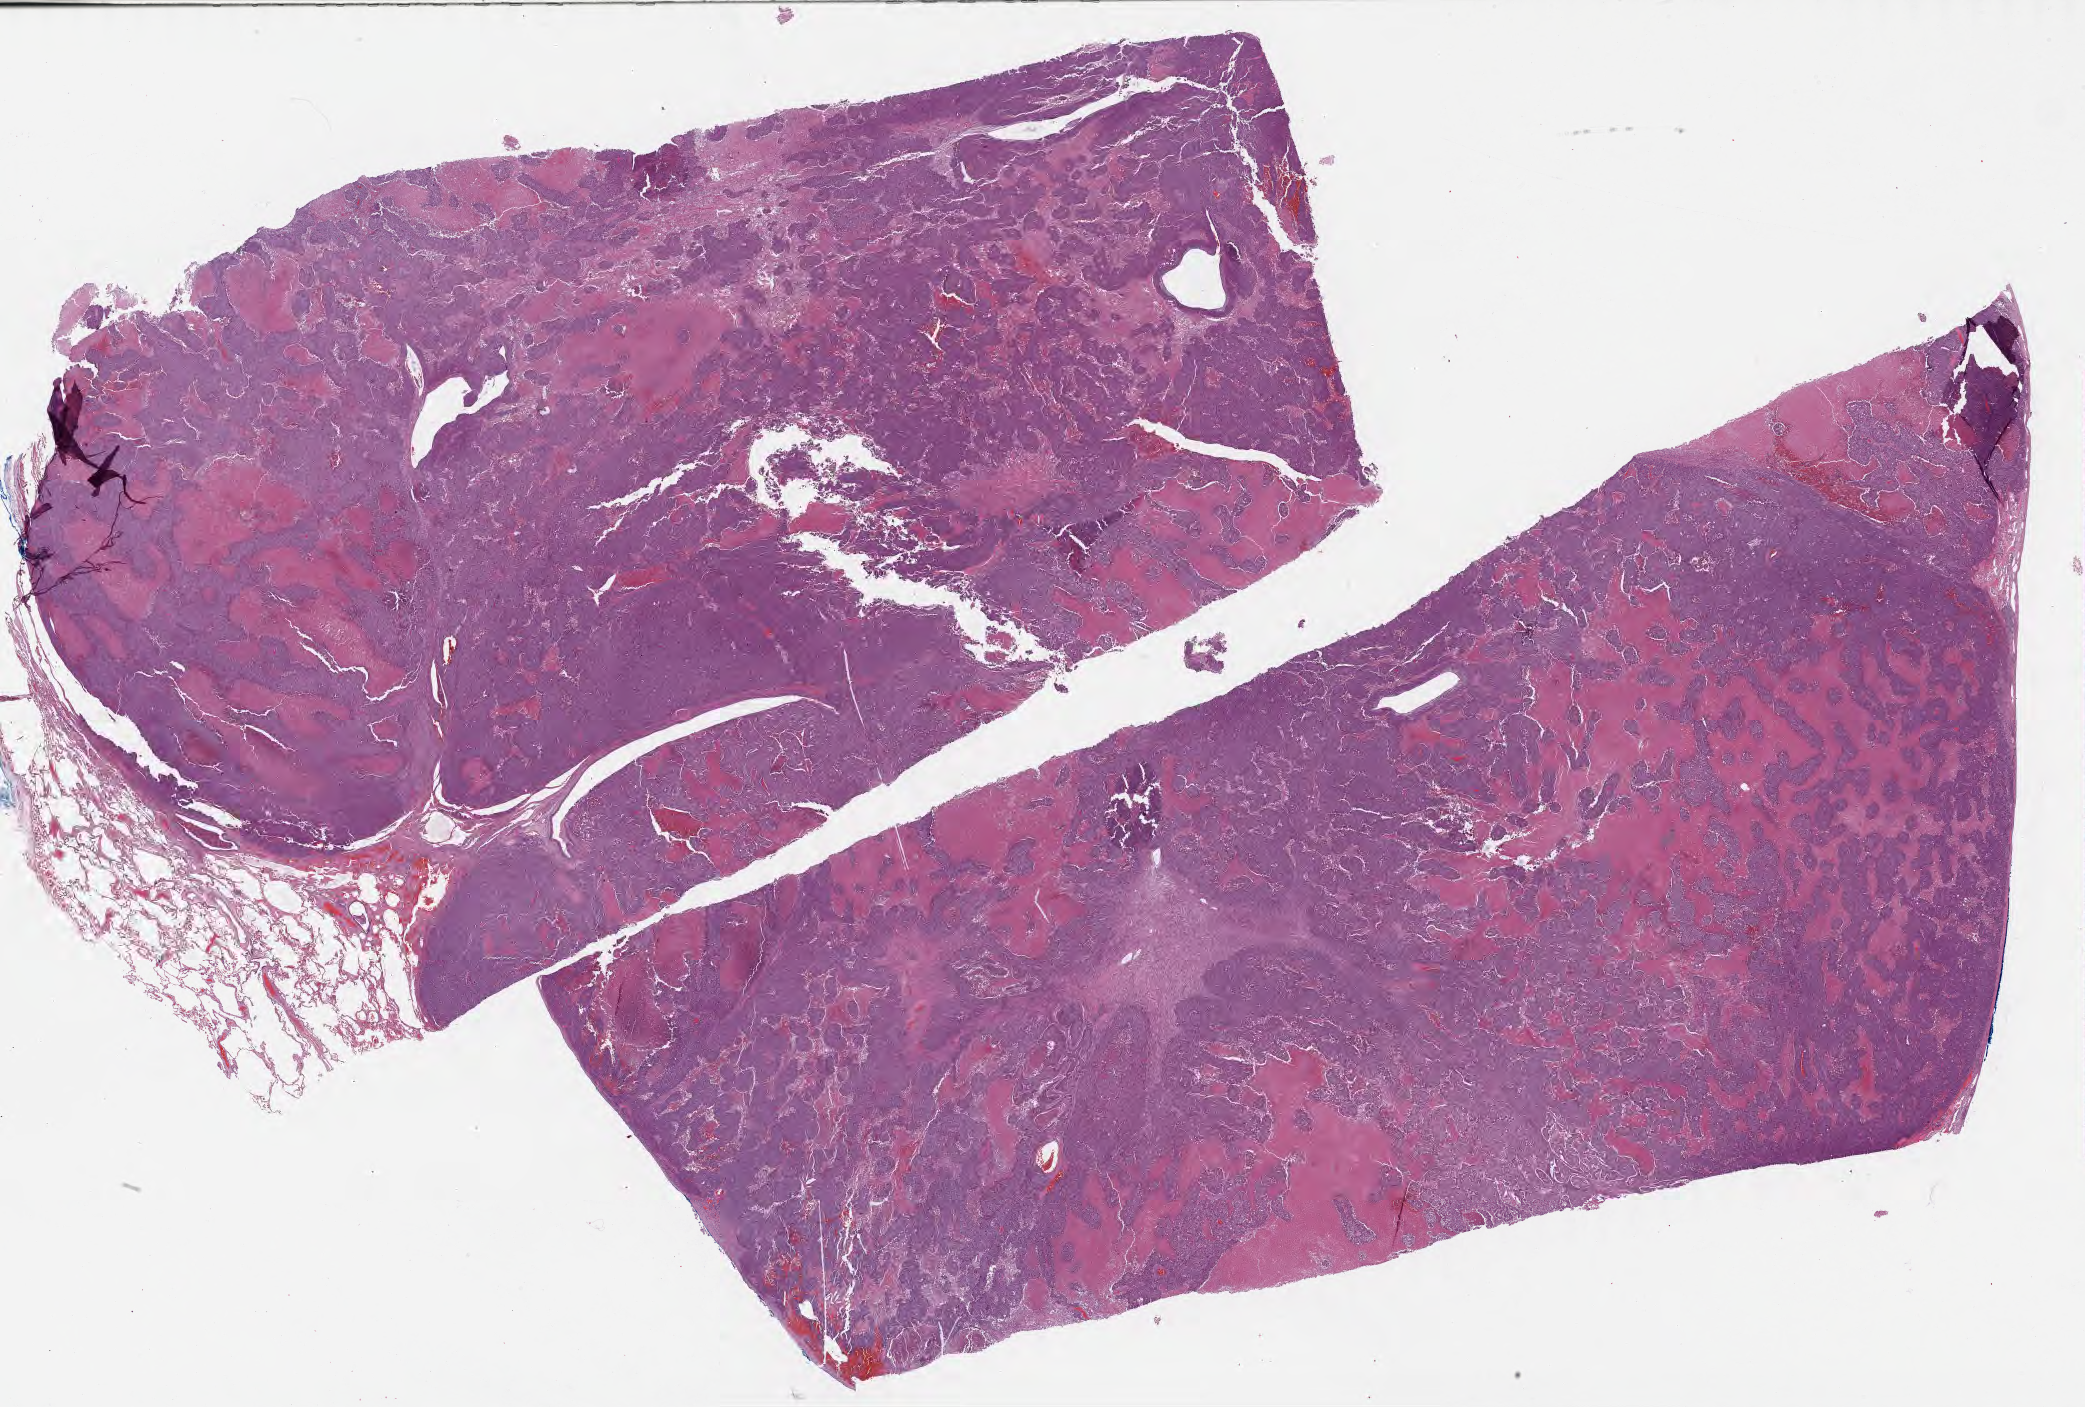
Haematoxylin and eosin whole-slide image, shown as a low-resolution overview of the whole scanned area (about 33.7 x 22.7 mm); tumor tissue; site: lung (right). Patient female; 61 years old.
• histologic diagnosis: Large cell neuroendocrine carcinoma